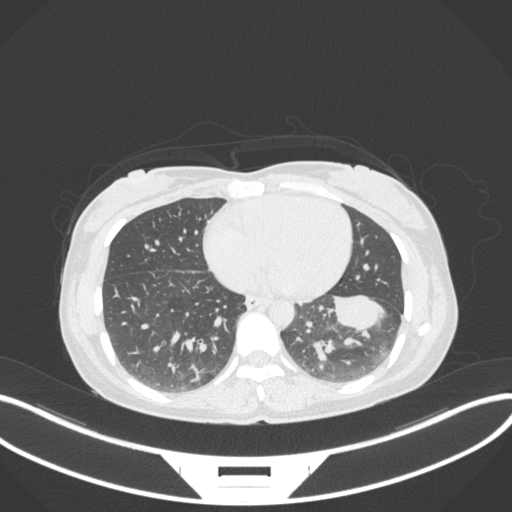
Chest CT, one axial slice; position 133 of 361 along the scan axis; reconstruction kernel B31f; 120 kVp; lung window (W 1500 / L -600 HU); 1 mm slice thickness; 512 × 512 image matrix. Patient: female, 41 years. Case-level facts recorded for this patient, not image findings: clinical TNM (as recorded): T2a N3 M1b.
Structures marked on this image (rectangle marked by the reading radiologist):
- lung tumour (recorded histology: adenocarcinoma): bounding box (x1, y1, x2, y2) in pixels: (328, 293, 398, 343)